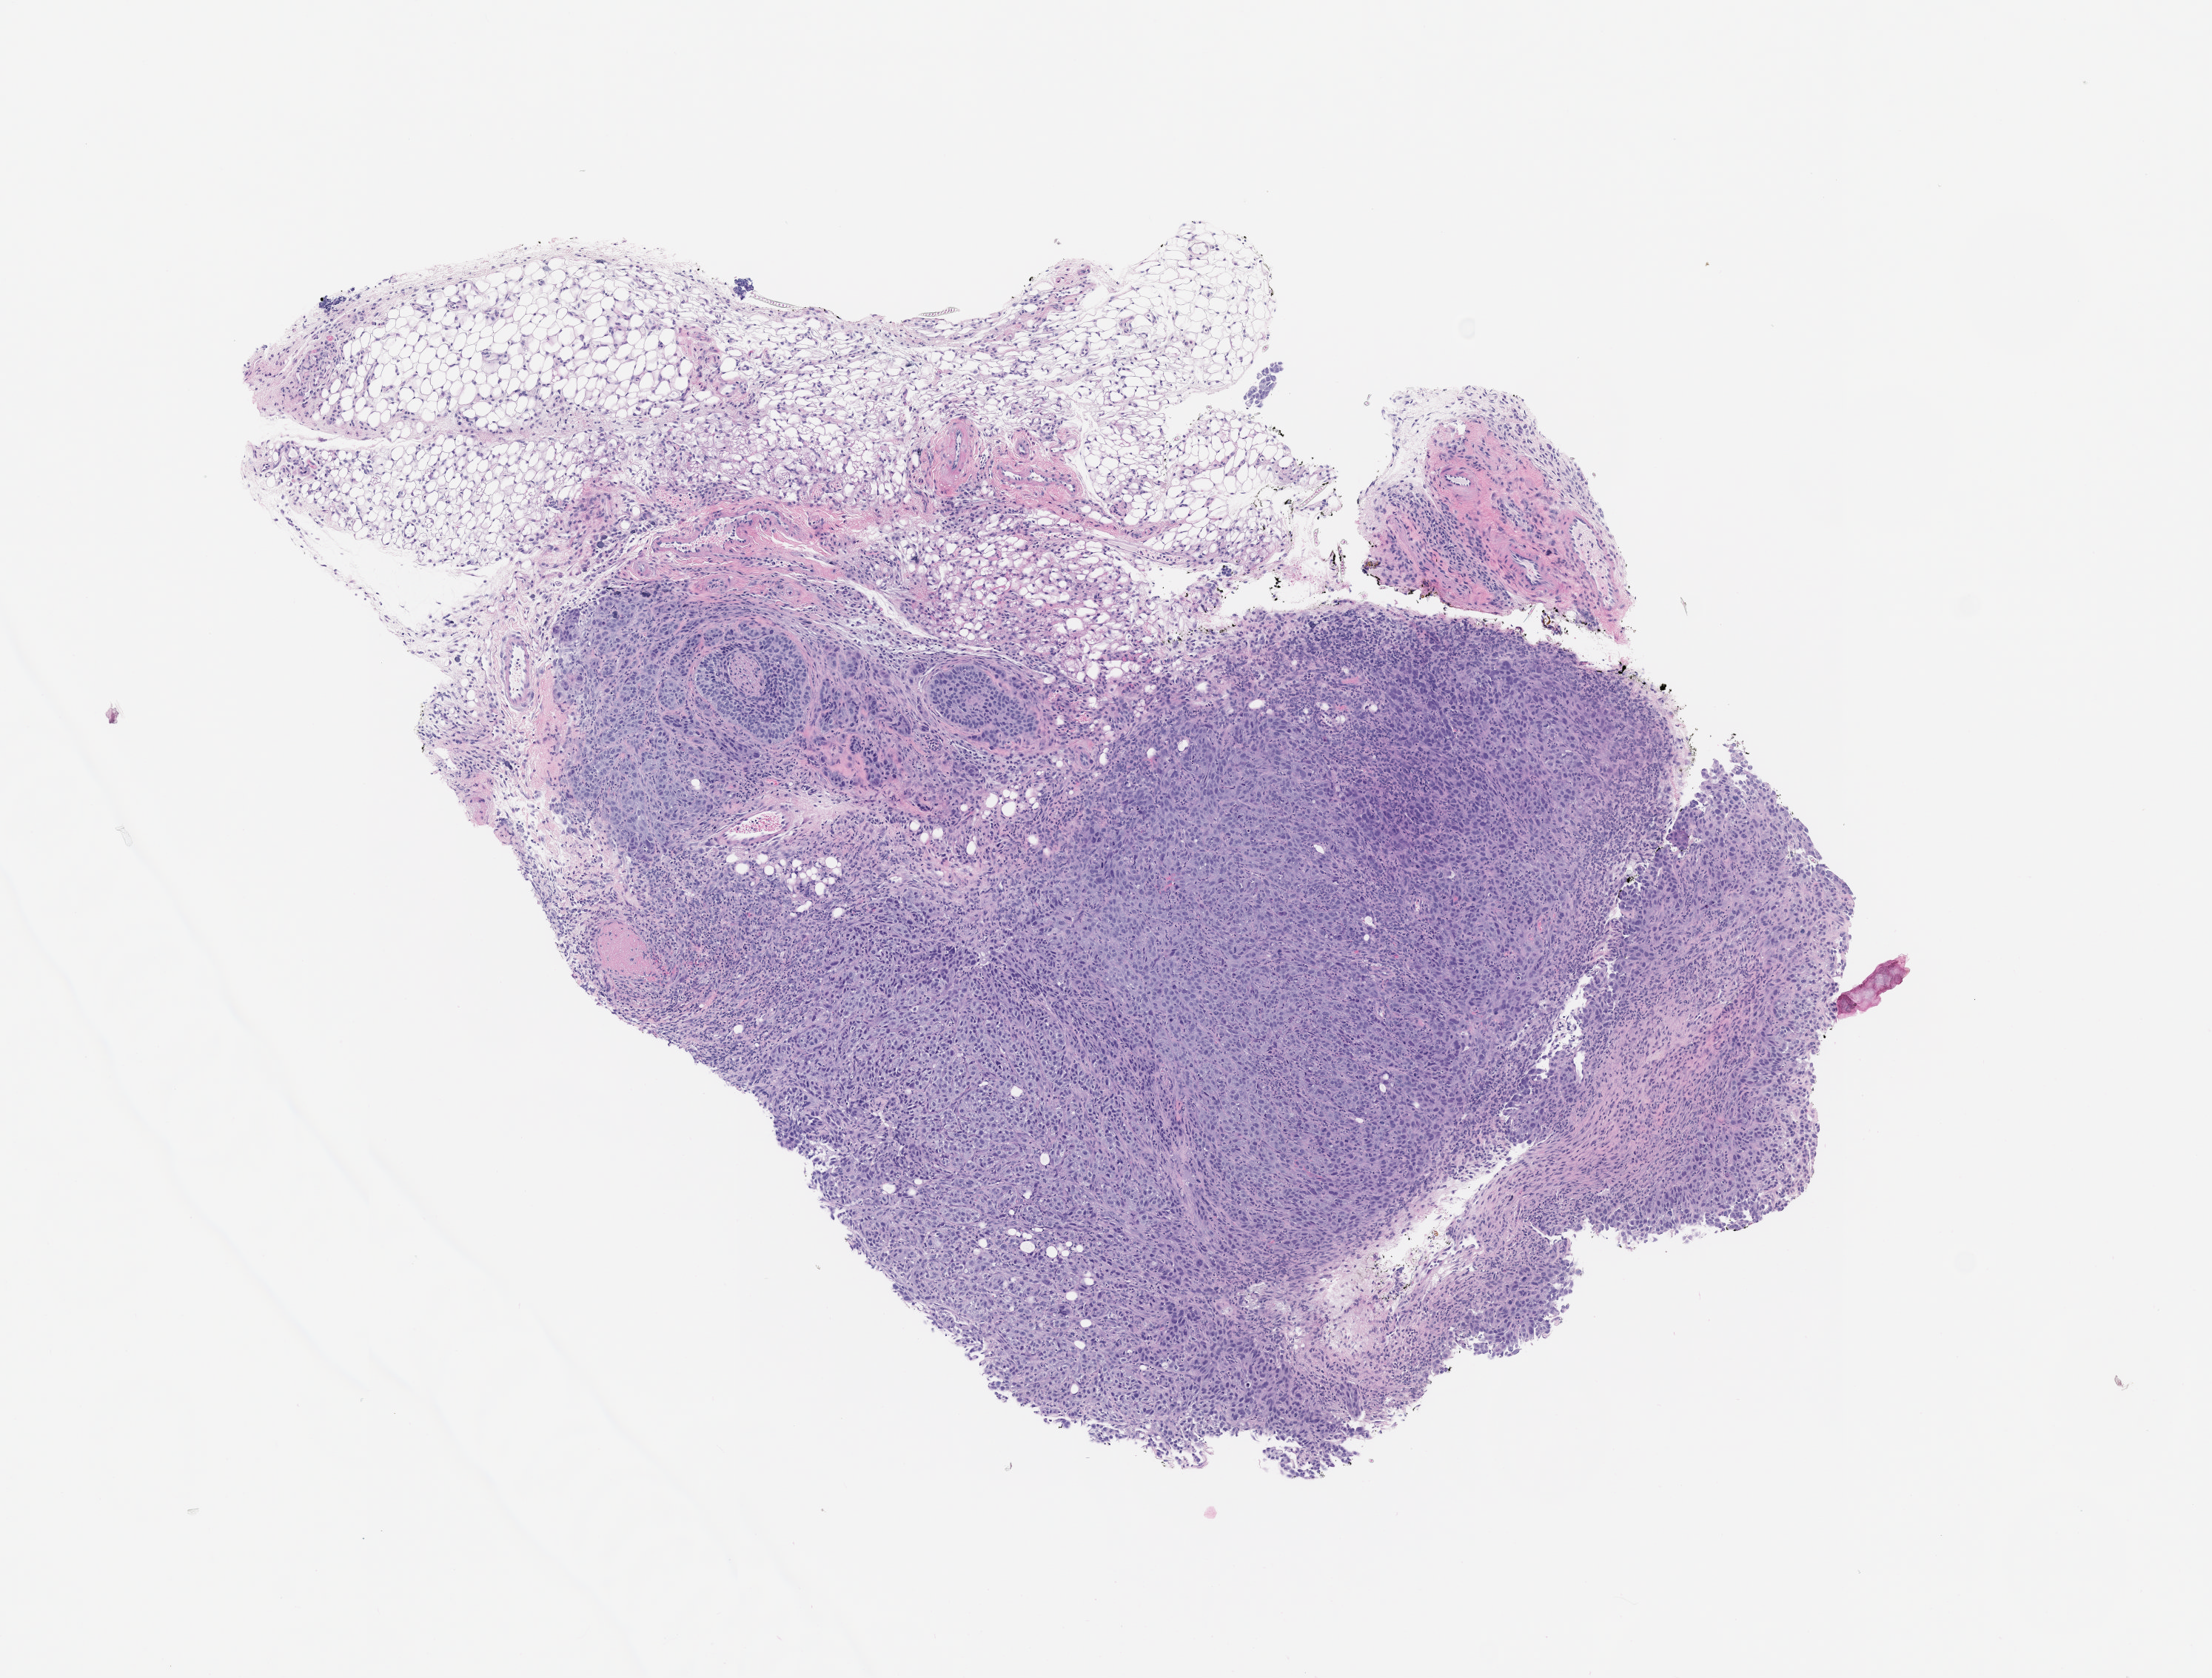
H&E whole-slide image of a patient-derived xenograft (PDX) tumor grown in a mouse, passage 4 — low-resolution overview of the scanned area, about 6.0 x 4.6 mm; FFPE section; originating tumor site category: bladder.
Originating patient diagnosis: Transitional Cell Carcinoma.